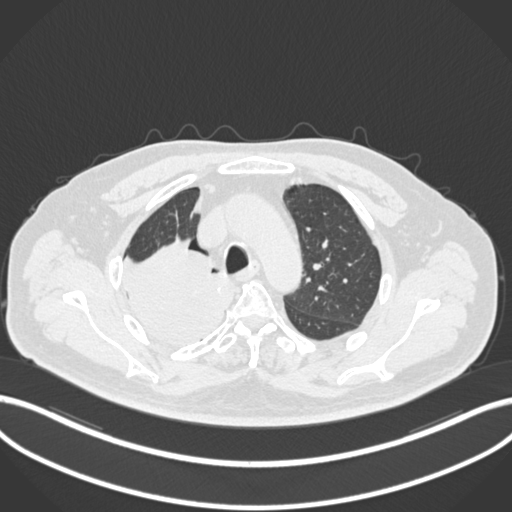
Chest CT, one axial slice. Reconstruction kernel B30f. 120 kVp. Lung window (W 1500 / L -600 HU). 1 mm slice thickness. 512 × 512 image matrix, field of view 400 × 400 mm. Patient: male, 68 years. From the clinical record (not read from this slice): clinical TNM (as recorded): T2a N0 M0.
Structures marked on this image (bounding box drawn by a radiologist):
- lung tumour (recorded histology: adenocarcinoma): bounding box (x1, y1, x2, y2) in pixels: (124, 238, 235, 341)